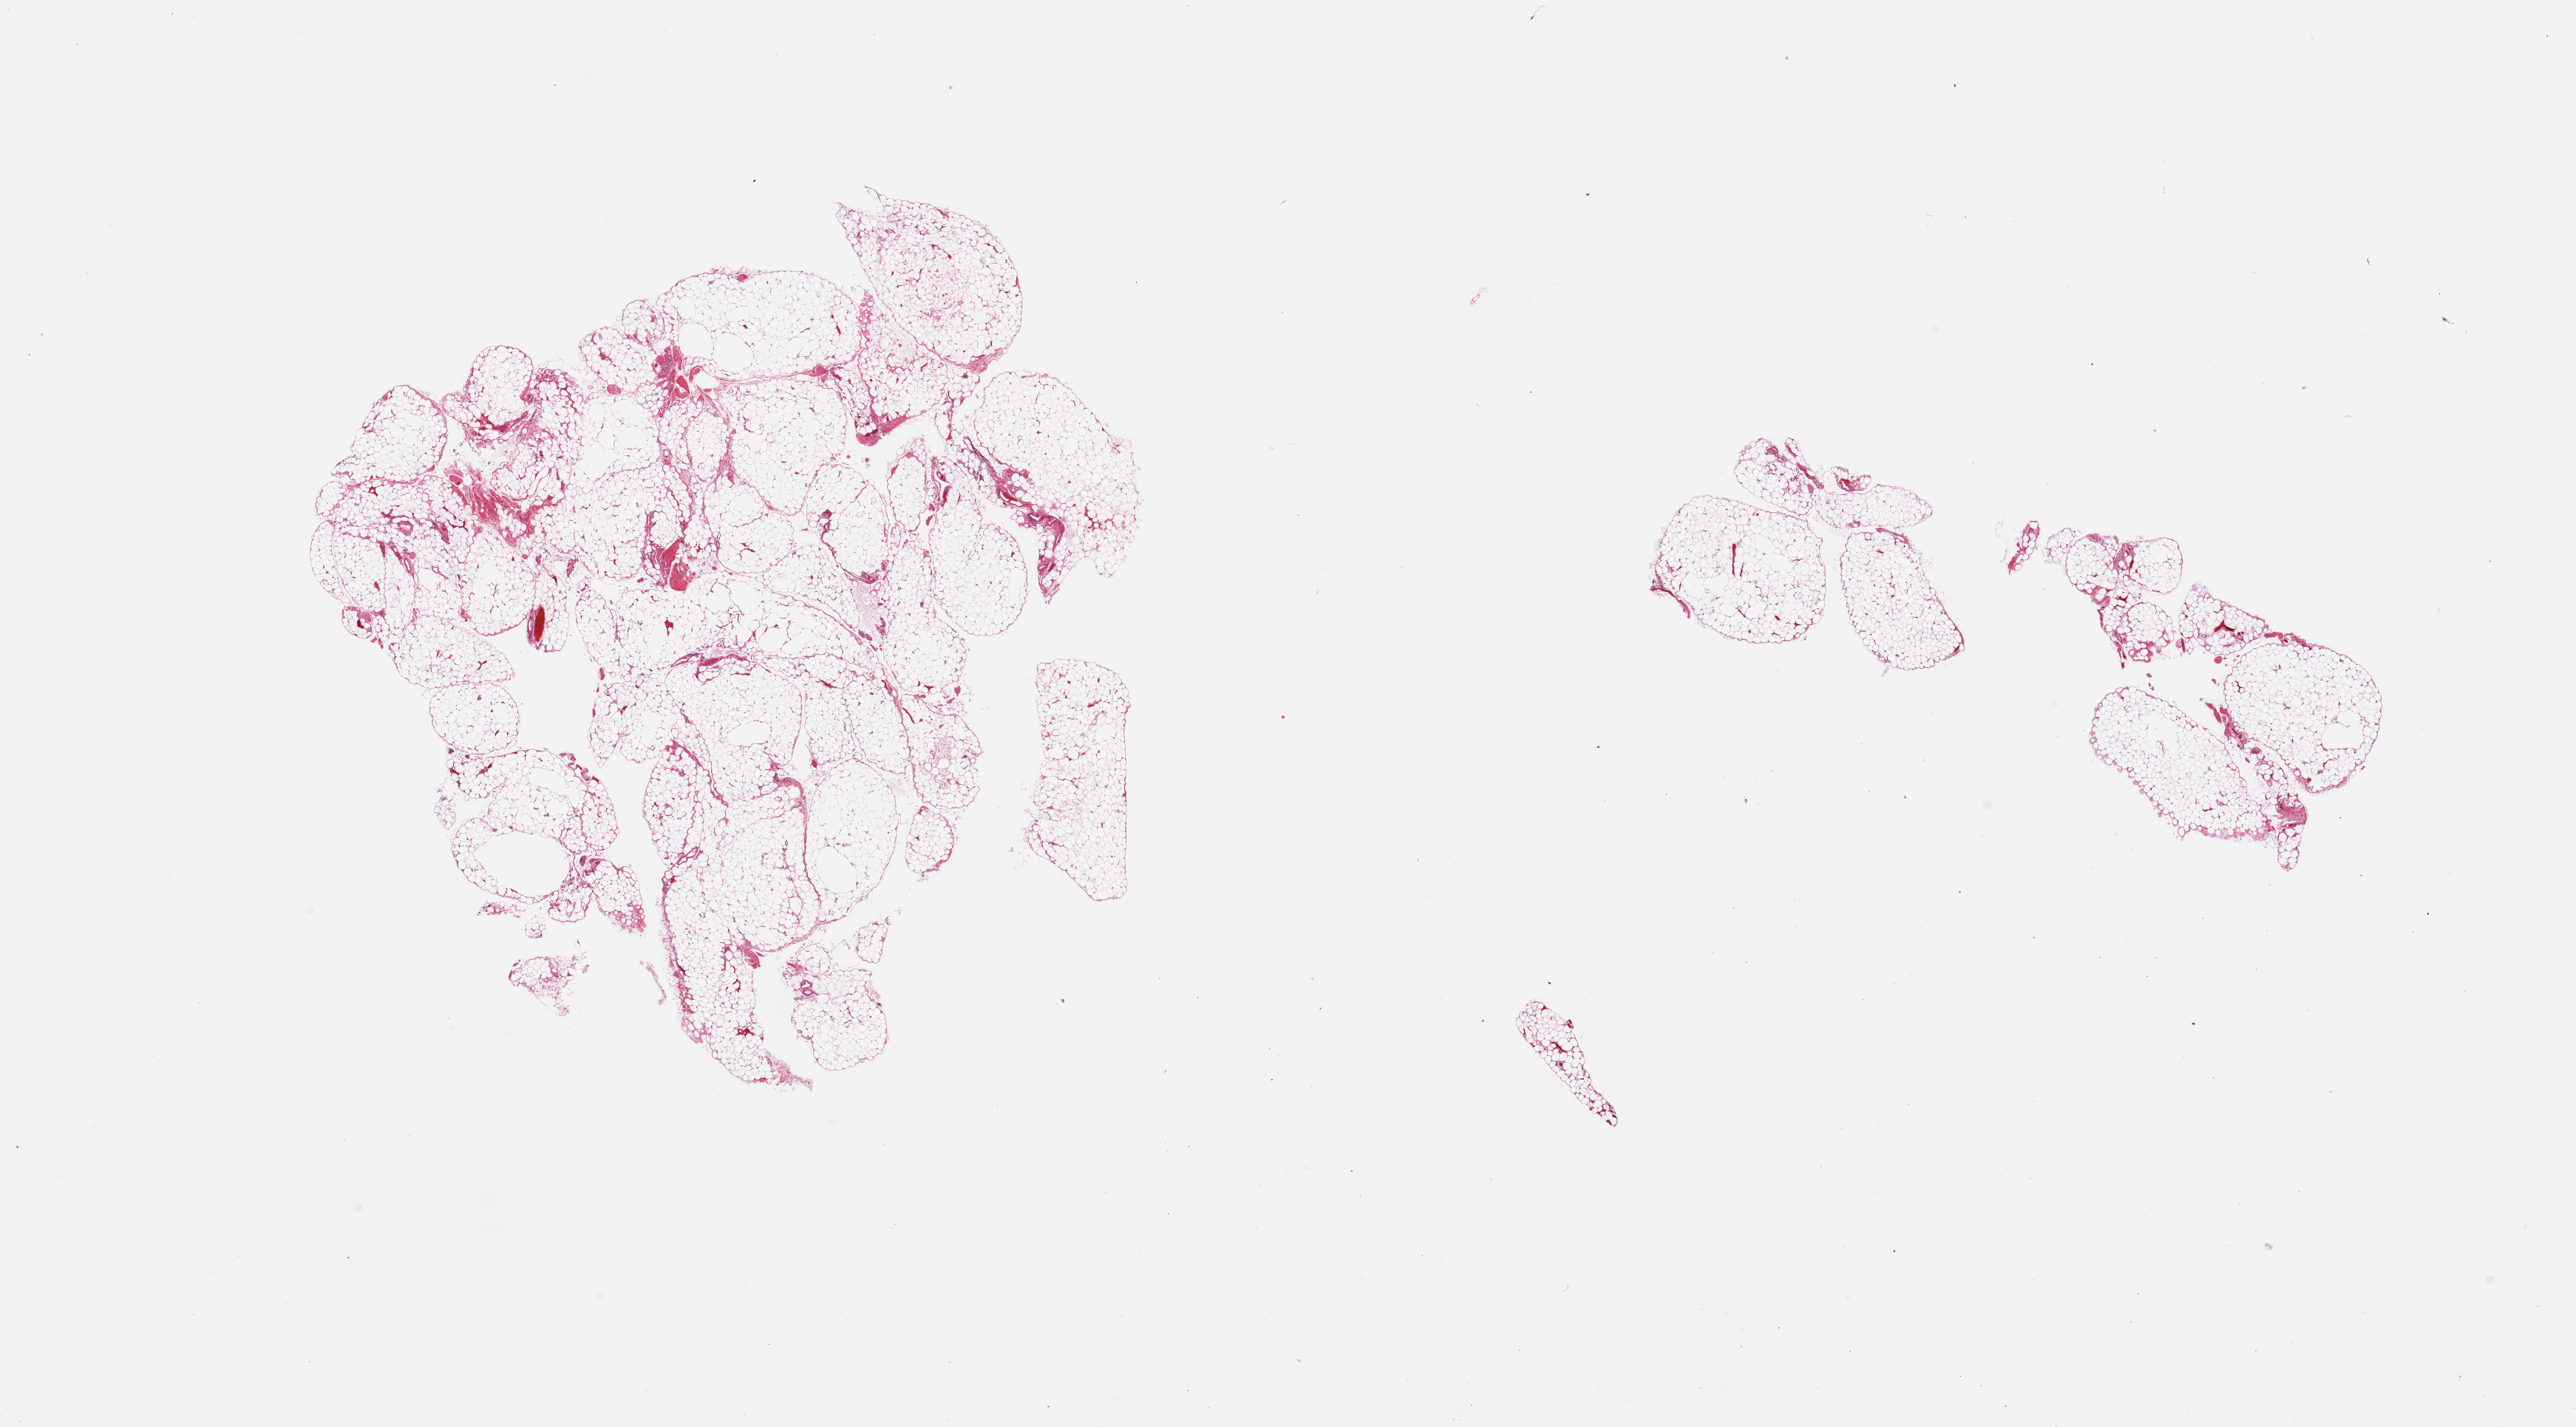
H&E whole-slide image, brightfield — shown as a low-resolution overview of the whole scanned area (about 27.6 x 15.3 mm). PAXgene-fixed paraffin-embedded (PFPE) section. Sampled site (target tissue): omentum. Donor tissue sample.
* reviewer comment on this tissue sample: 2 pieces; lobulated mature adipose tissue and fibrovascular component